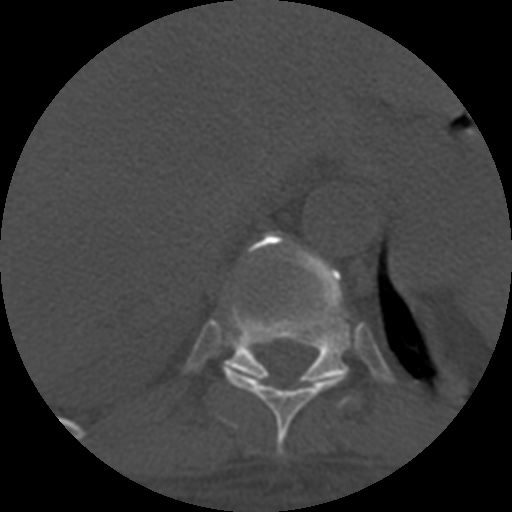
CT including the spine, one axial slice. Position 347 of 708 along the scan axis. 120 kVp. One of 3 acquisitions stored at this slice position. Bone window (W 1800 / L 400 HU). 1.25 mm slice thickness. 512 × 512 image matrix, field of view 160 × 160 mm. Patient age 55 years. From the clinical record (not read from this slice): primary cancer: colon; vertebrae with lytic lesions (as recorded): T12, L1, L5.
Structures marked on this image (semi-automatically segmented with operator editing):
- T10 vertebra: bounding box <224,369,340,456> (left, top, right, bottom; pixels)
- T11 vertebra: <223,231,350,407>